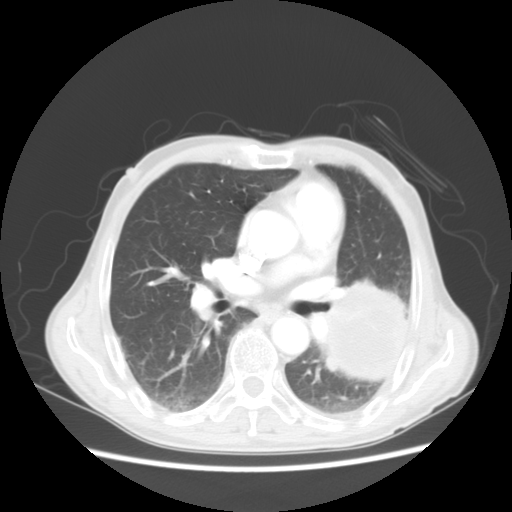
Chest CT, one axial slice. Position 27 of 51 along the scan axis. Reconstruction kernel STANDARD. Lung window (W 1500 / L -600 HU). 5 mm slice thickness. 512 × 512 image matrix. Patient: male, 64 years. From the clinical record (not read from this slice): clinical TNM (as recorded): T4 N0 M0.
Annotated regions visible in this slice (rectangle marked by the reading radiologist):
- lung tumour (recorded histology: squamous cell carcinoma): box from (x=326, y=283) to (x=408, y=382) px